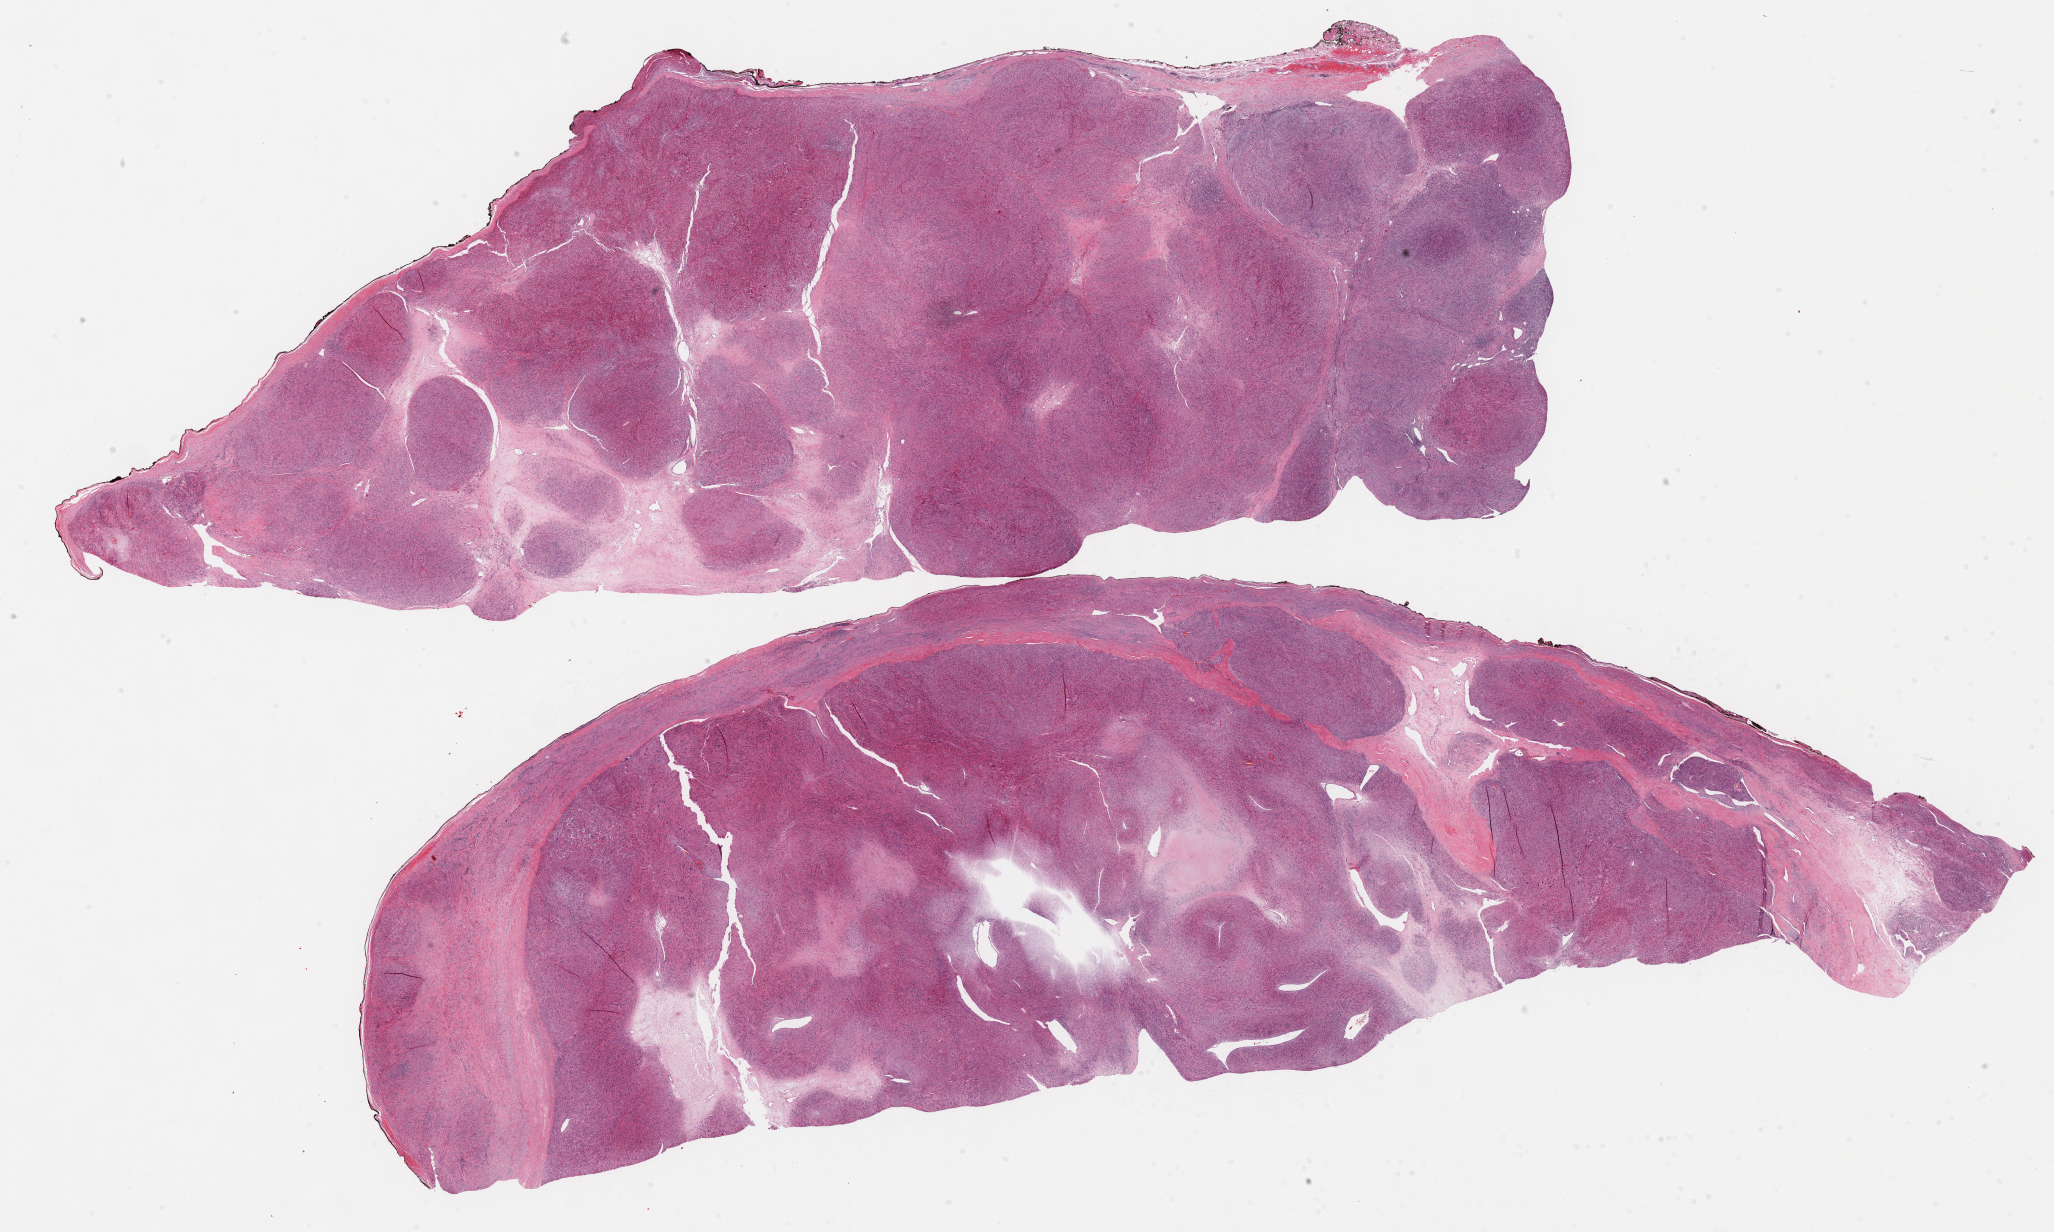
Digitized Hematoxylin and eosin (H&E) stained tissue section (whole slide) — a low-resolution overview of the entire scanned area, about 33.2 x 19.9 mm, formalin-fixed paraffin-embedded (FFPE) diagnostic section, primary tumour sample from the retroperitoneum and peritoneum. Female, age 56 years at initial diagnosis.
* histologic diagnosis: Leiomyosarcoma, NOS